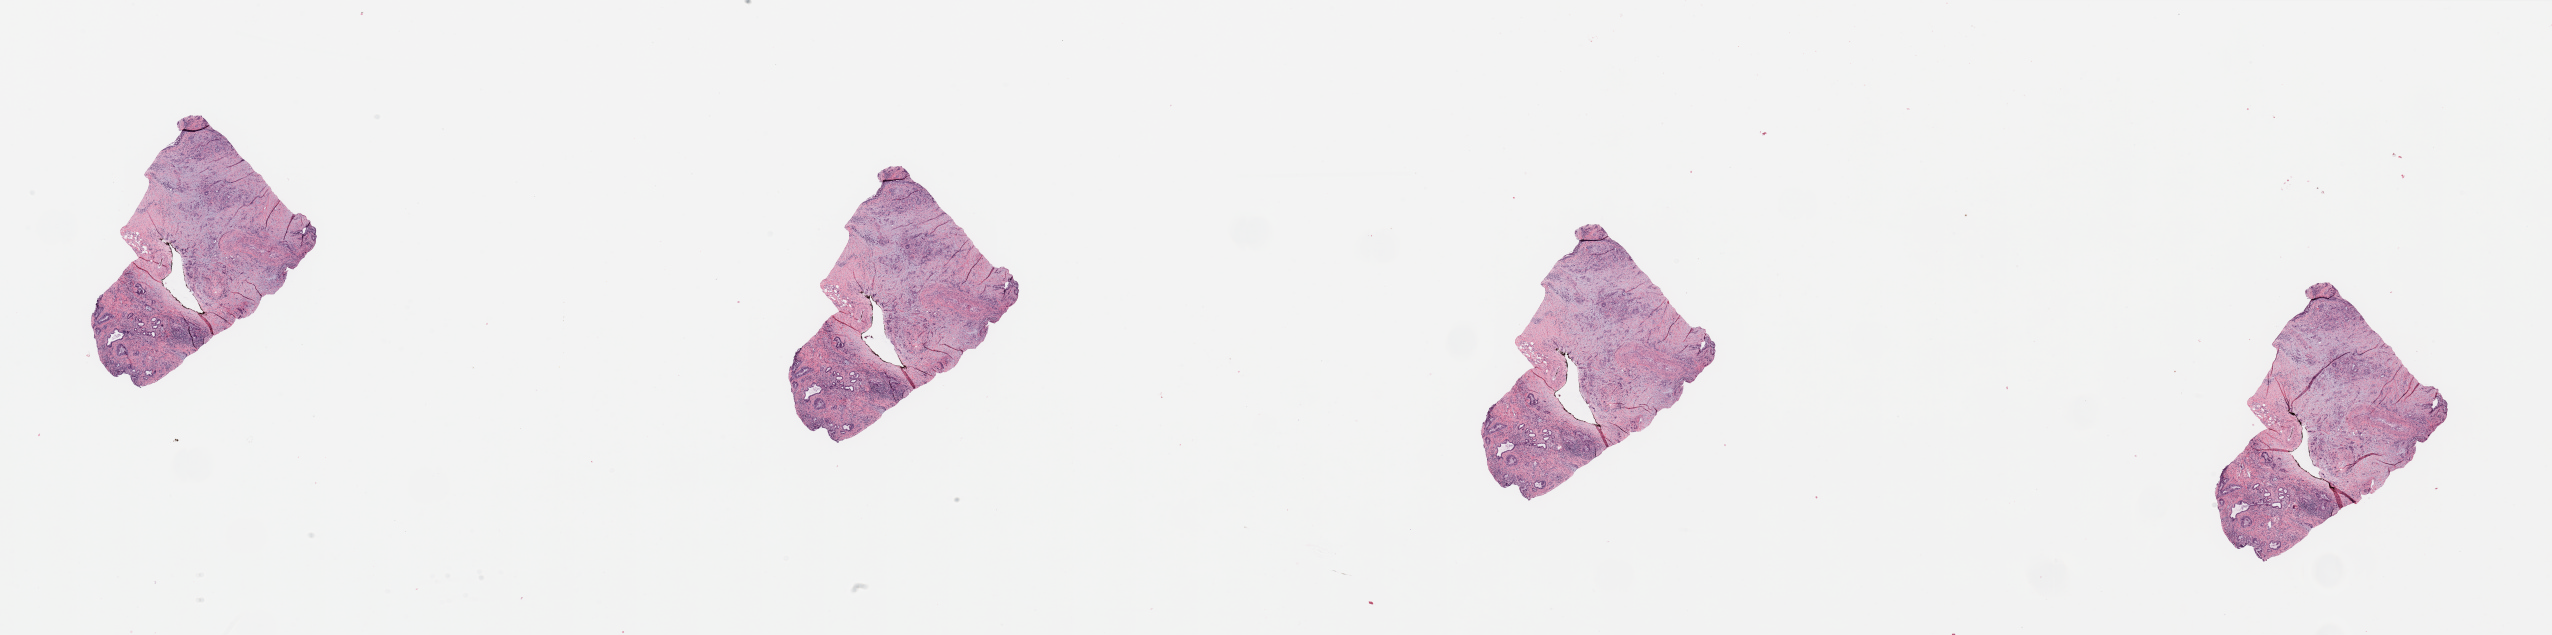
Digitized H&E-stained tissue section (whole slide), whole scanned area (about 40.4 x 10.0 mm, slide scanned at 20x) shown as a low-resolution overview. Tumour tissue sample, pancreas. Female, 67 y/o. Histologic grade: G2 (moderately differentiated).
AJCC pathologic stage: IB. Histologic diagnosis: Infiltrating duct carcinoma, NOS. Primary tumour site (as recorded): head.